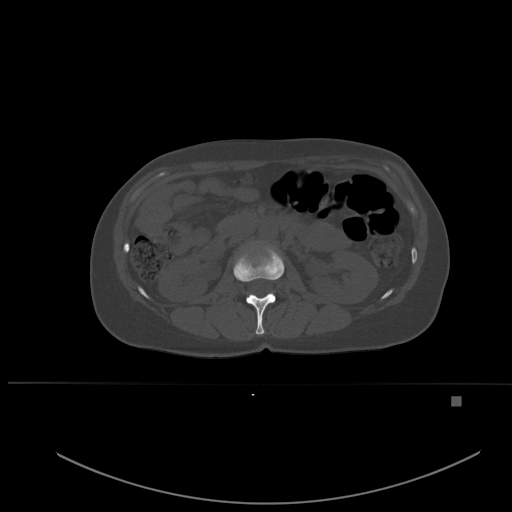
CT including the spine, one axial slice. Slice 228 of 651 in the series (ordered by position). Bone window (W 1800 / L 400 HU). 512 × 512 image matrix. Female patient, age 49 years. Case-level facts recorded for this patient, not image findings: primary cancer: breast; vertebrae with lytic lesions (as recorded): L3, T12, L4.
Annotated regions visible in this slice (semi-automatic segmentation, software-assisted and operator-edited):
- L1 vertebra: bounding box <233,246,285,335> (left, top, right, bottom; pixels)